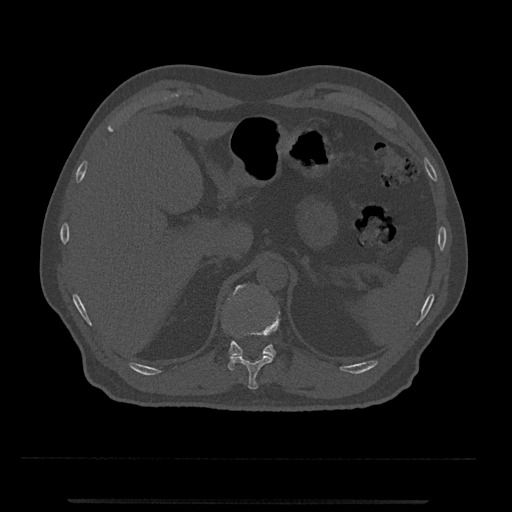
CT including the spine, one axial slice; slice 437 of 797 in the series (ordered by position); reconstruction kernel Br40s/3; 120 kVp; bone window (W 1800 / L 400 HU); 0.5 mm slice thickness; 512 × 512 image matrix, field of view 419 × 419 mm. Male patient, age 63 years. From the clinical record (not read from this slice): primary cancer: prostate.
Outlined on this slice (semi-automatic segmentation, software-assisted and operator-edited):
- T11 vertebra: bounding box <230,310,280,390> (left, top, right, bottom; pixels)
- T12 vertebra: <225,285,276,371>